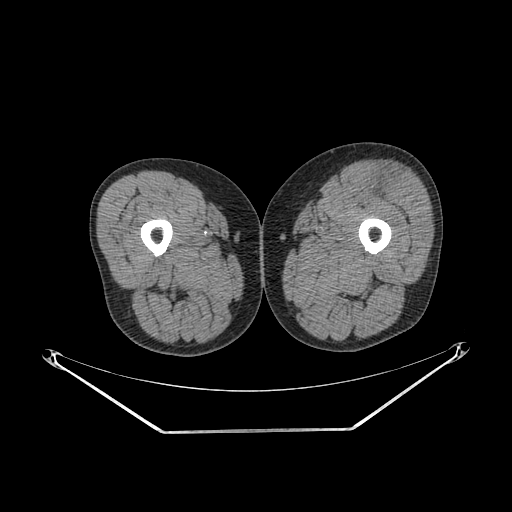
CT of an extremity soft-tissue mass (from a PET/CT study), one axial slice. Position 221 of 267 along the scan axis. 140 kVp. Soft-tissue window (W 400 / L 40 HU). 3.75 mm slice thickness. 512 × 512 image matrix. Male patient. From the clinical record (not read from this slice): histological type: extraskeletal osteosarcoma; grade: high; site of the primary tumour: thigh.
Annotated regions visible in this slice (expert contour drawn on MRI and transferred to this co-registered scan by the dataset authors):
- gross tumour volume (mass): bounding box (x1, y1, x2, y2) in pixels: (377, 174, 405, 204)